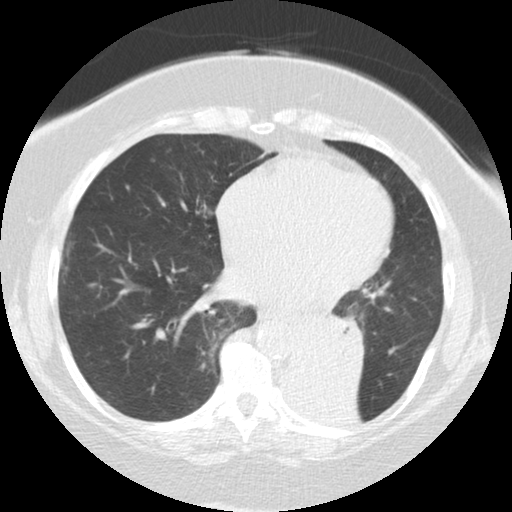
Chest CT (low-dose screening protocol), one axial image; baseline screening round; lung window (W 1500 / L -600 HU); 2.5 mm slice thickness; 120 kVp; 512 × 512 image matrix, field of view 309 × 309 mm. Female, age 71 years at enrolment. Former smoker at enrolment.
Lesion marked by an expert reader, box from (x=280, y=302) to (x=369, y=383) px. Reader record for this screening exam (exam-level; its link to the box is not recorded): non-calcified nodule or mass ≥4 mm, right middle lobe, 5 × 5 mm, smooth margins, soft tissue attenuation. Note: the box lies in the patient's left hemithorax on this image, whereas the reader's record names the right lung; they may be different findings. Participant outcome: lung cancer diagnosed 46 days after this screen — large cell carcinoma, NOS, left lower lobe, mediastinum, other location, poorly differentiated (G3), stage IV (AJCC 6th edition), 50 mm at pathology.